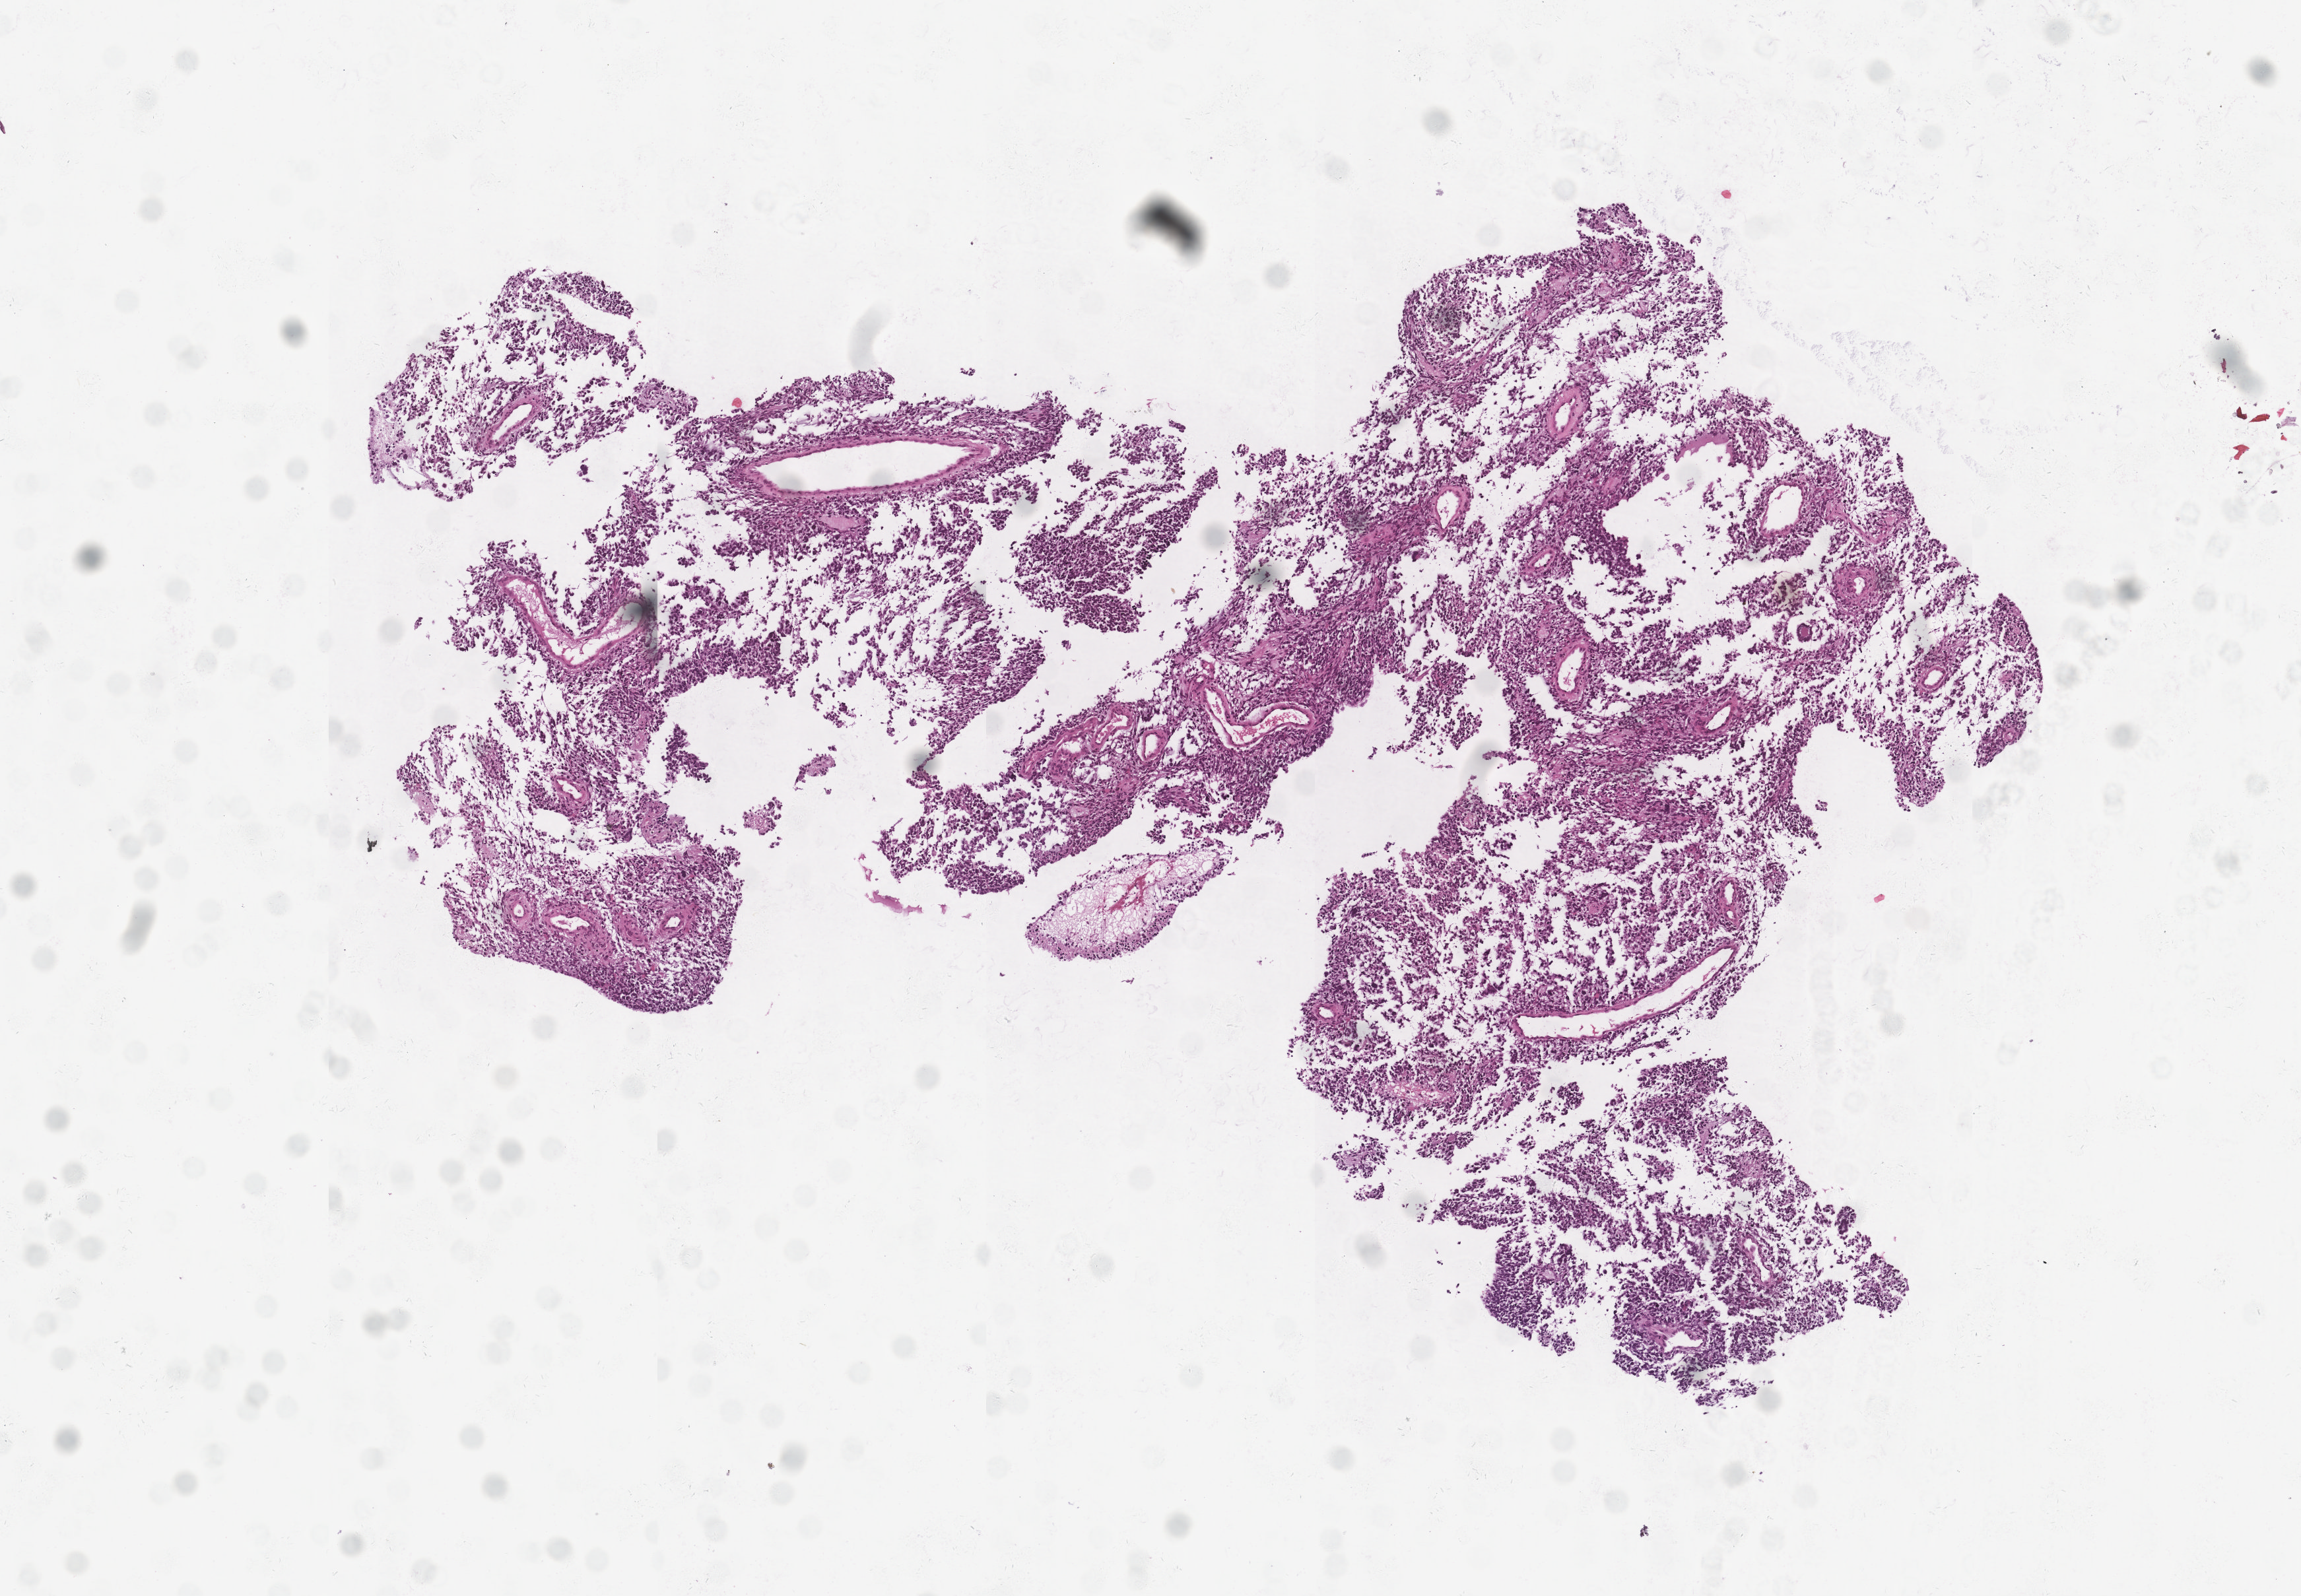
Whole-slide histology image, Hematoxylin and eosin (H&E) stained, whole scanned area (about 7.0 x 4.9 mm, acquisition: 20x scan) shown as a low-resolution overview, tumour tissue sample, brain. Patient: female, age 29 years.
Diagnosis: Glioblastoma.